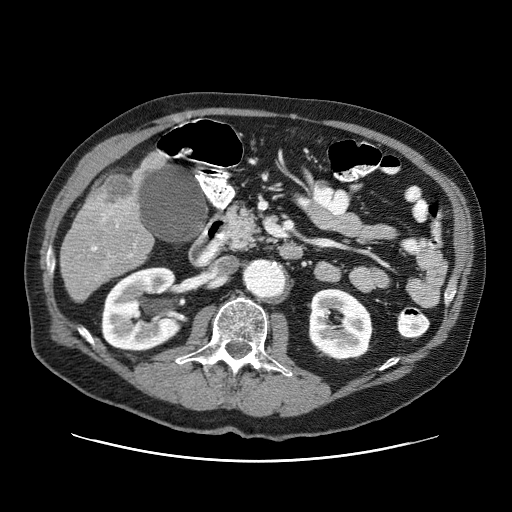
Contrast-enhanced abdominal CT (liver protocol), one axial slice. Position 20 of 87 along the scan axis. Reconstruction kernel STANDARD. 120 kVp. One of 3 acquisitions stored at this slice position. Soft-tissue window (W 400 / L 40 HU). 2.5 mm slice thickness. 512 × 512 image matrix. Case-level facts recorded for this patient, not image findings: diagnosis: hepatocellular carcinoma (patient treated with transarterial chemoembolisation; whether this scan precedes or follows treatment is not stated here); TNM stage (as recorded): Stage-IIIA; Child-Pugh class: A; tumour differentiation: well differentiated; tumour nodularity: multinodular.
Outlined on this slice (semi-automatically segmented with operator editing):
- liver parenchyma outside the tumour (the mass and vessels are separate outlines, so this box may not span the whole liver): bounding box <60,150,166,302> (left, top, right, bottom; pixels)
- mass: <85,173,138,221>
- liver vessels: <91,153,164,257>